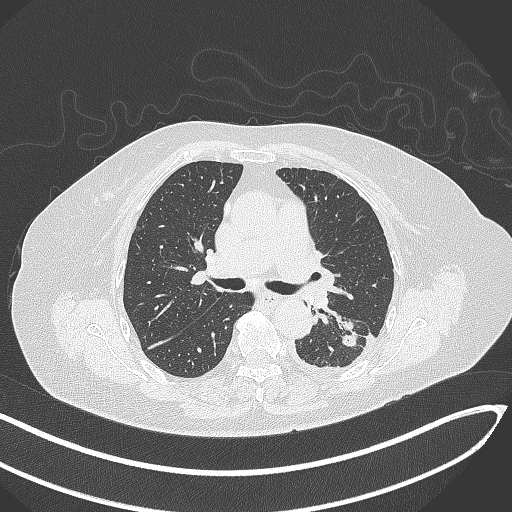
Chest CT, one axial slice; position 192 of 270 along the scan axis; reconstruction kernel B70f; 120 kVp; lung window (W 1500 / L -600 HU); 1 mm slice thickness; 512 × 512 image matrix, field of view 400 × 400 mm. Patient: female, 76 years. Case-level facts recorded for this patient, not image findings: clinical TNM (as recorded): T1c N0 M0.
Outlined on this slice (bounding box drawn by a radiologist):
- lung tumour (recorded histology: adenocarcinoma): bounding box (x1, y1, x2, y2) in pixels: (338, 318, 360, 349)